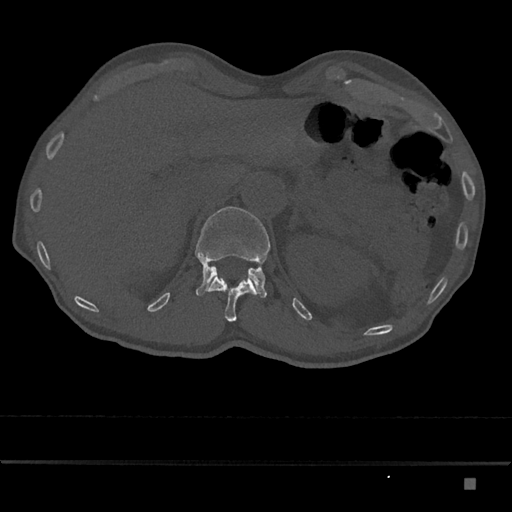
CT including the spine, one axial slice; position 579 of 797 along the scan axis; reconstruction kernel Br40s/3; 120 kVp; bone window (W 1800 / L 400 HU); 0.5 mm slice thickness; 512 × 512 image matrix, field of view 390 × 390 mm. Male patient, age 72 years. Case-level facts recorded for this patient, not image findings: primary cancer: prostate.
Outlined on this slice (semi-automatically segmented with operator editing):
- L1 vertebra: bounding box [x1, y1, x2, y2] px = [195, 206, 270, 298]
- T12 vertebra: [205, 275, 256, 322]